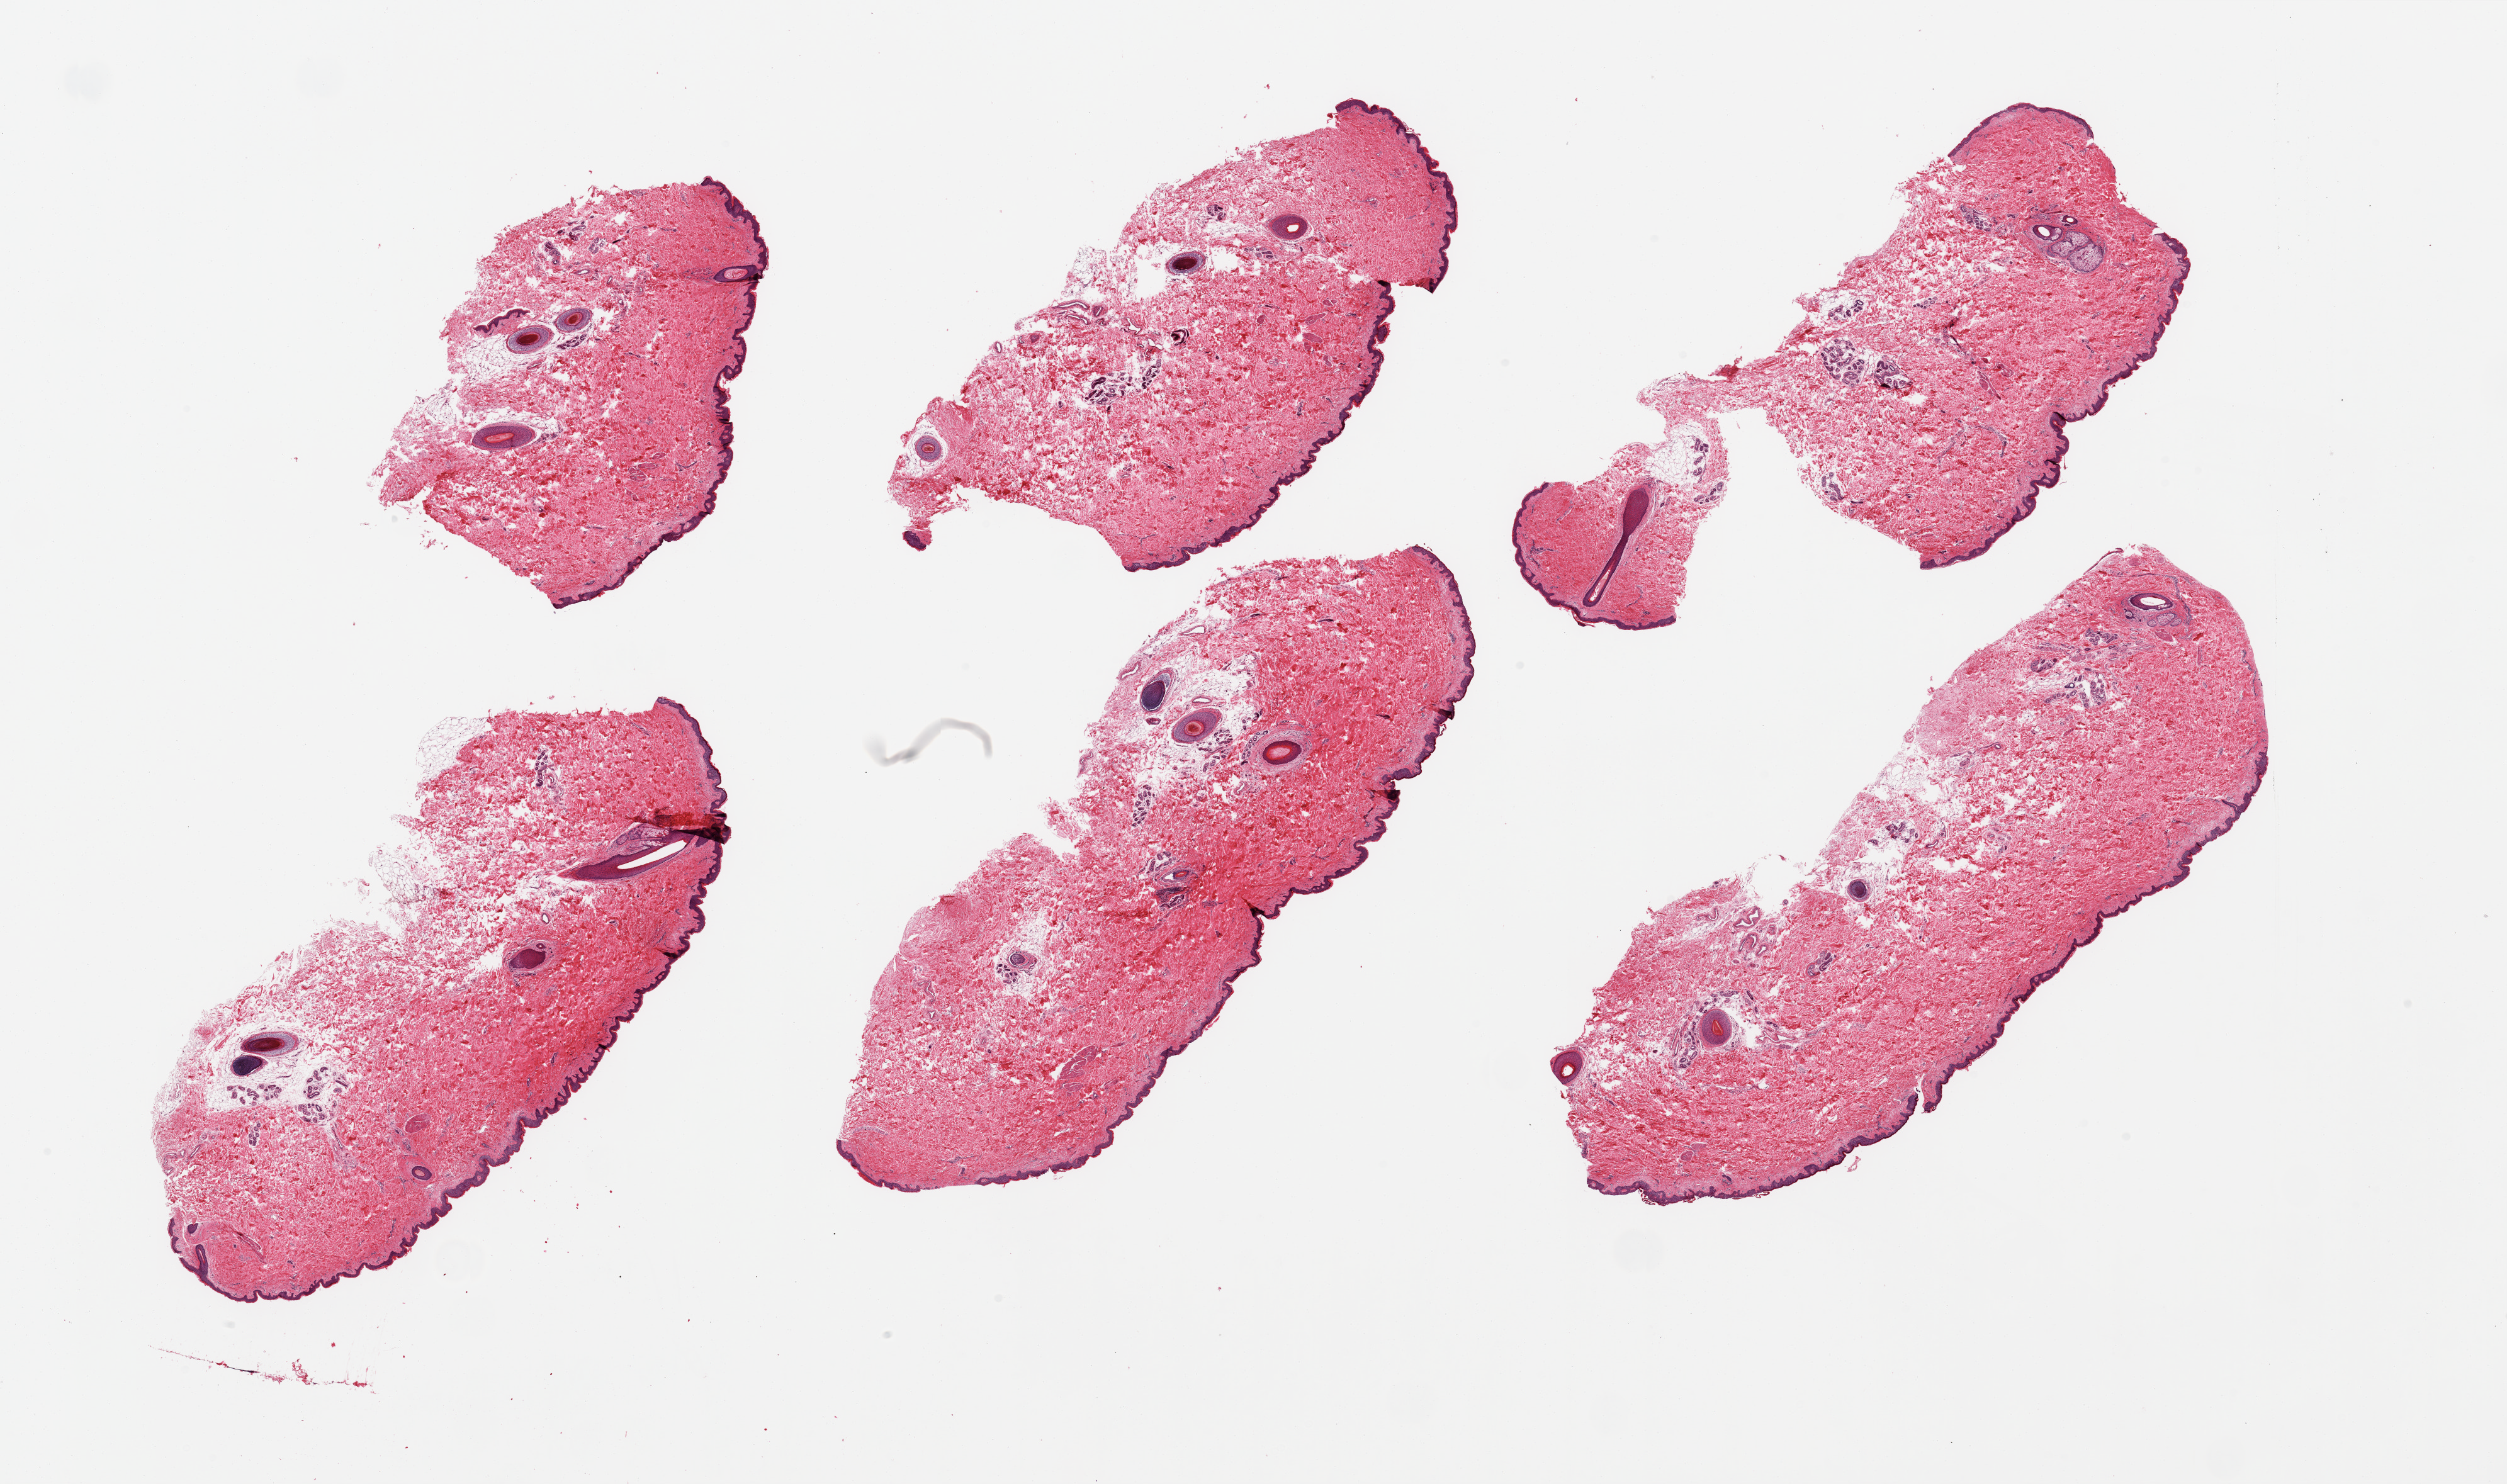
Whole-slide image, hematoxylin and eosin (H&E) stain — shown as a low-resolution overview of the whole scanned area (about 31.5 x 18.6 mm); PAXgene-fixed, paraffin-embedded tissue; target tissue: skin of suprapubic region; tissue donor sample. Donor: male.
* reviewer comment on this tissue sample: 6 pieces, minimal dermal fat; squamous epithelium is ~50 microns